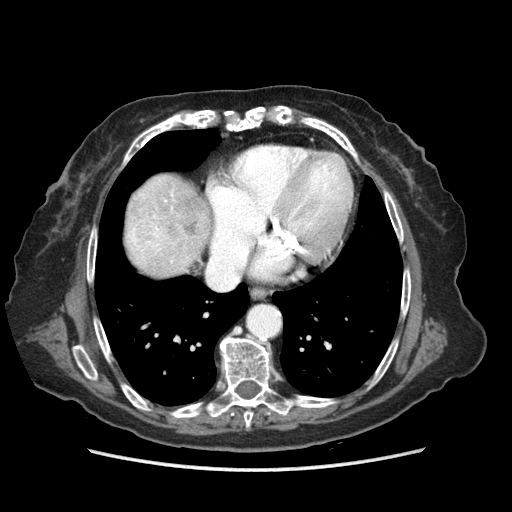
Contrast-enhanced abdominal CT (liver protocol), one axial slice. Reconstruction kernel STANDARD. Soft-tissue window (W 400 / L 40 HU). 2.5 mm slice thickness. 512 × 512 image matrix, field of view 360 × 360 mm. Case-level facts recorded for this patient, not image findings: diagnosis: hepatocellular carcinoma (patient treated with transarterial chemoembolisation; whether this scan precedes or follows treatment is not stated here); TNM stage (as recorded): Stage-IIIA; Child-Pugh class: A.
Annotated regions visible in this slice (semi-automatic segmentation, software-assisted and operator-edited):
- liver parenchyma outside the tumour (the mass and vessels are separate outlines, so this box may not span the whole liver): box from (x=124, y=174) to (x=210, y=276) px
- mass: (x=166, y=221)–(x=198, y=237)
- liver vessels: (x=130, y=227)–(x=160, y=250)